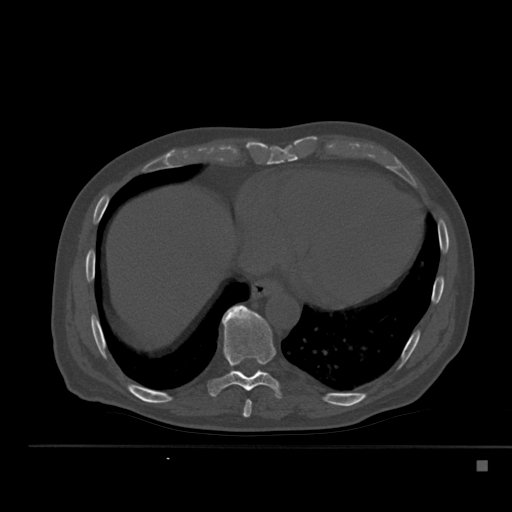
CT including the spine, one axial slice; position 288 of 517 along the scan axis; reconstruction kernel Br40s; 120 kVp; bone window (W 1800 / L 400 HU); 512 × 512 image matrix. Patient: male, 70 years. Case-level facts recorded for this patient, not image findings: primary cancer: renal.
Outlined on this slice (semi-automatically segmented with operator editing):
- T8 vertebra: box from (x=243, y=400) to (x=252, y=418) px
- T9 vertebra: (x=208, y=305)–(x=282, y=399)